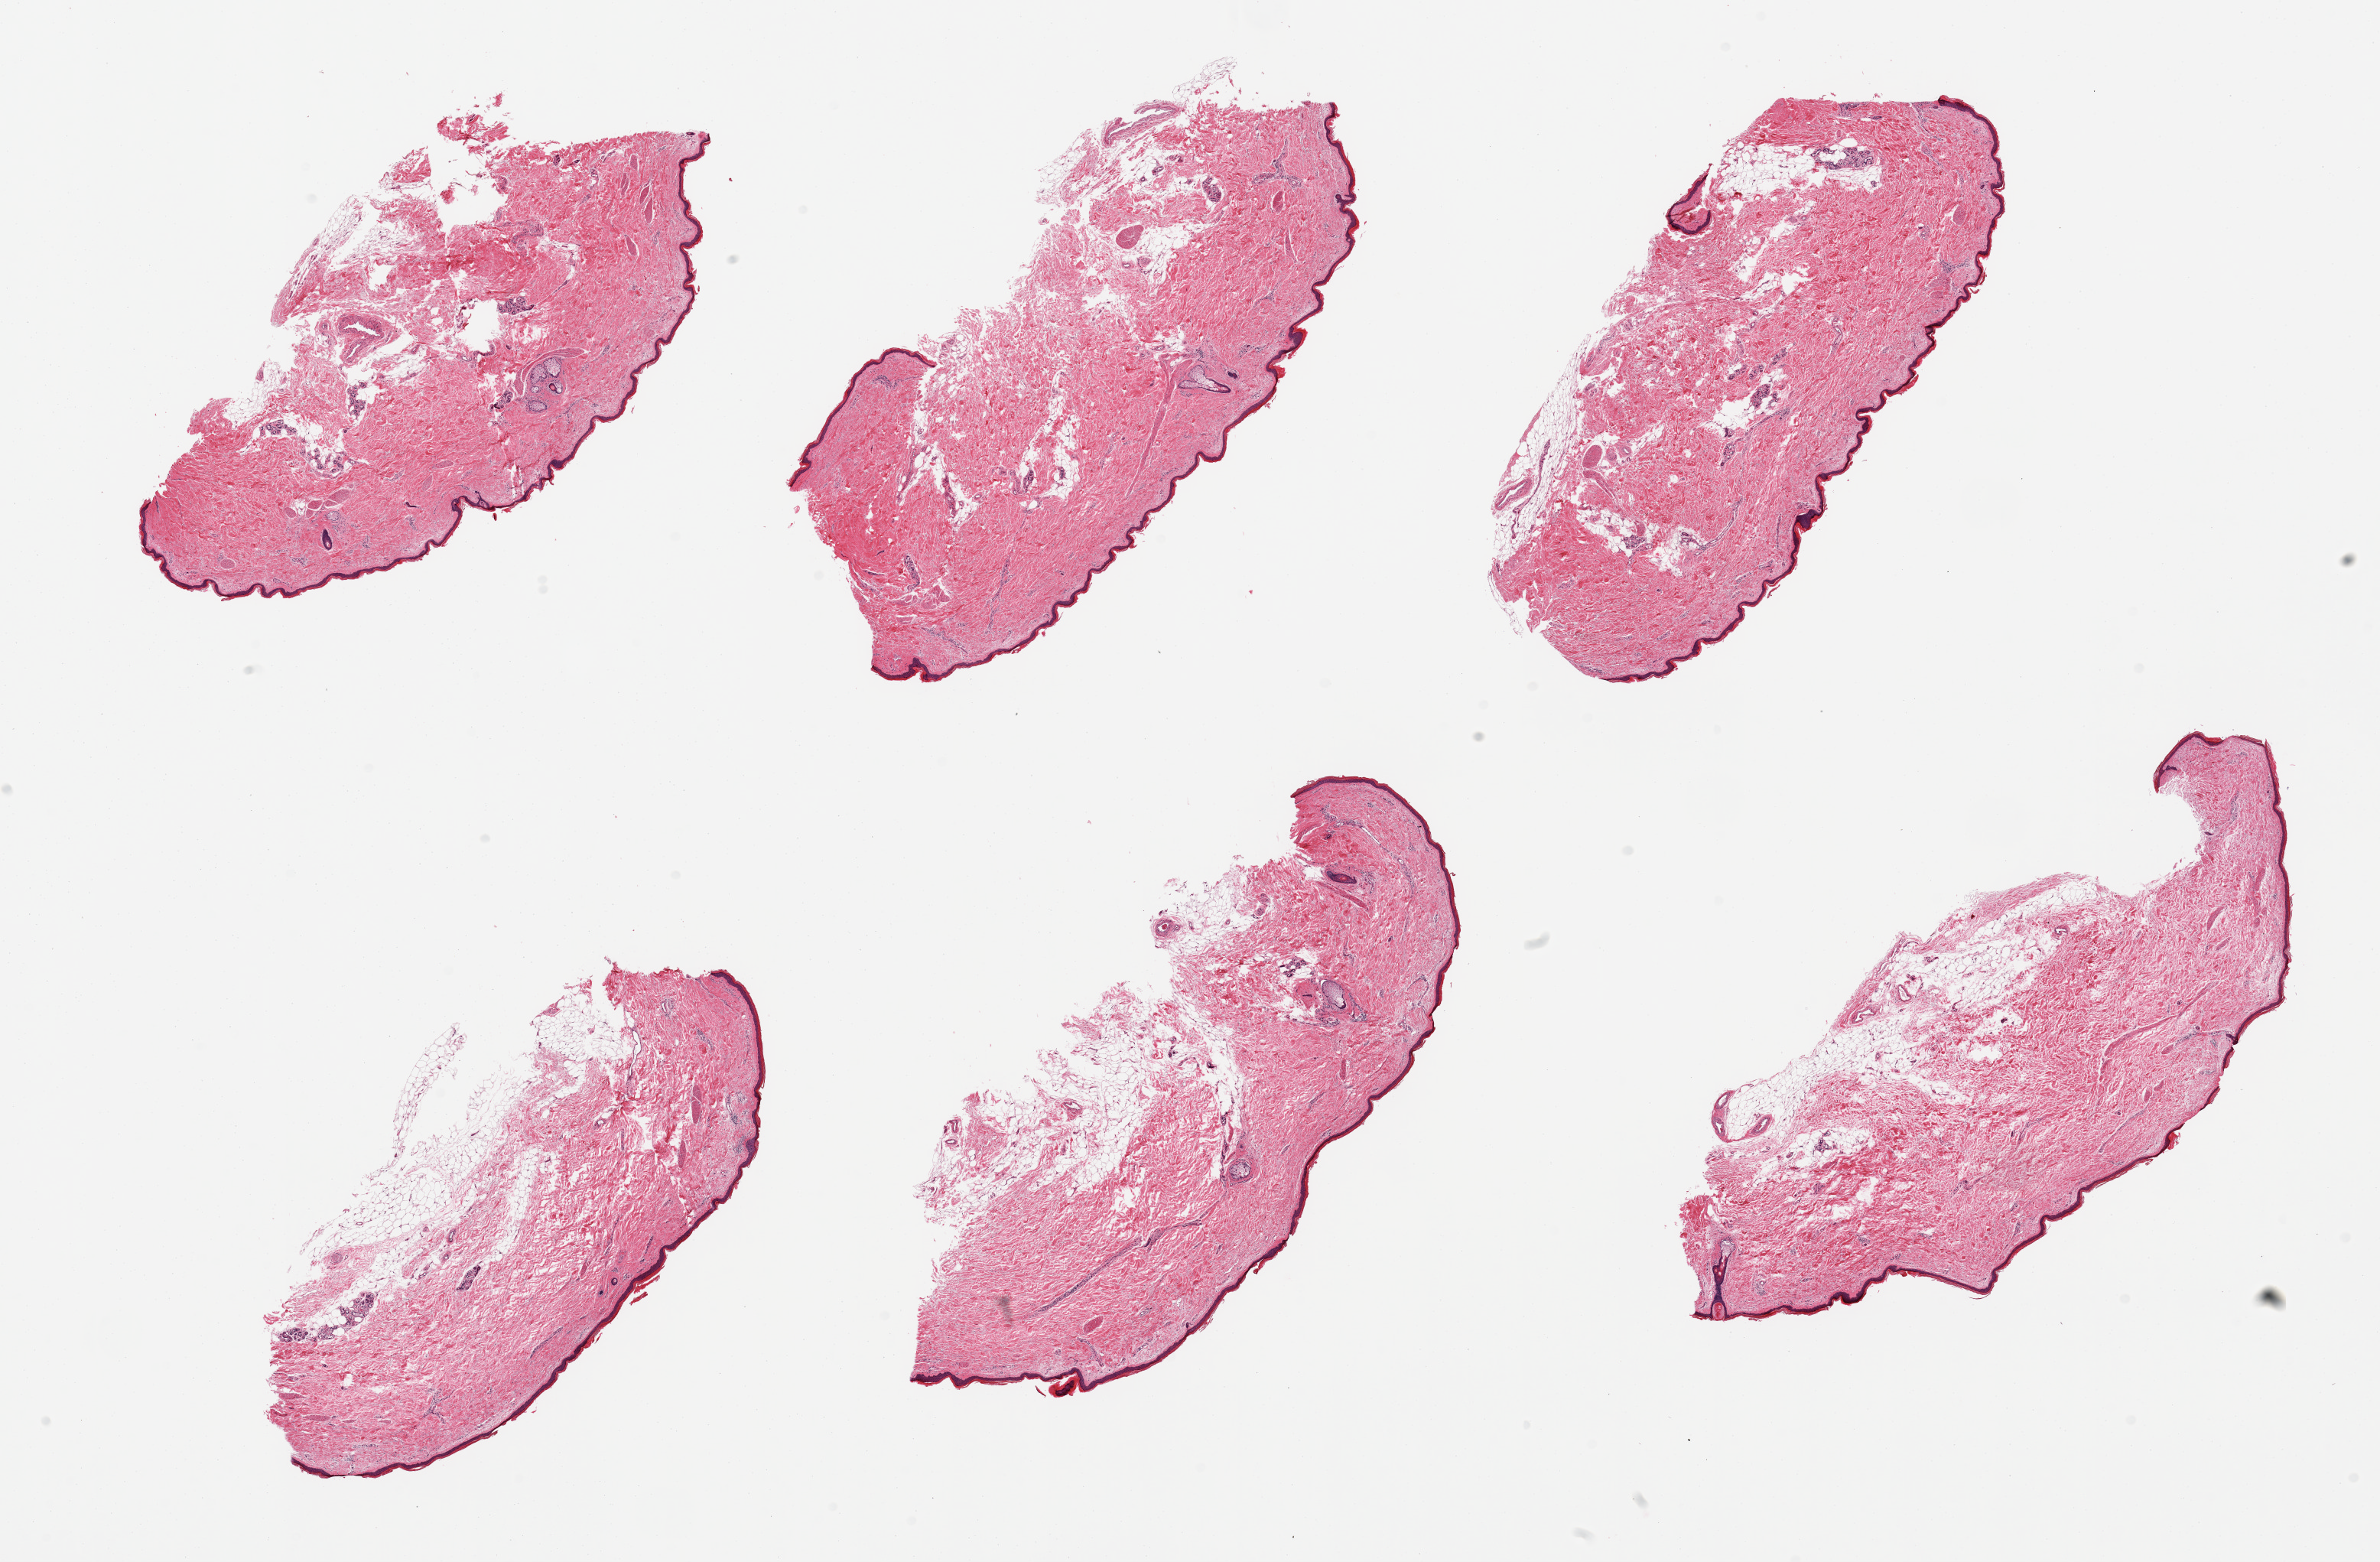
Digitized haematoxylin and eosin-stained section, low-resolution overview of the scanned area, about 24.6 x 16.1 mm (slide scanned at 20x), PAXgene-fixed, paraffin-embedded tissue, target tissue: skin of lower leg, tissue donor sample. Donor sex: male.
Reviewer comment on this tissue sample: 6 pieces; 10 - 20% external/internal fat, epidermis 31um thick.